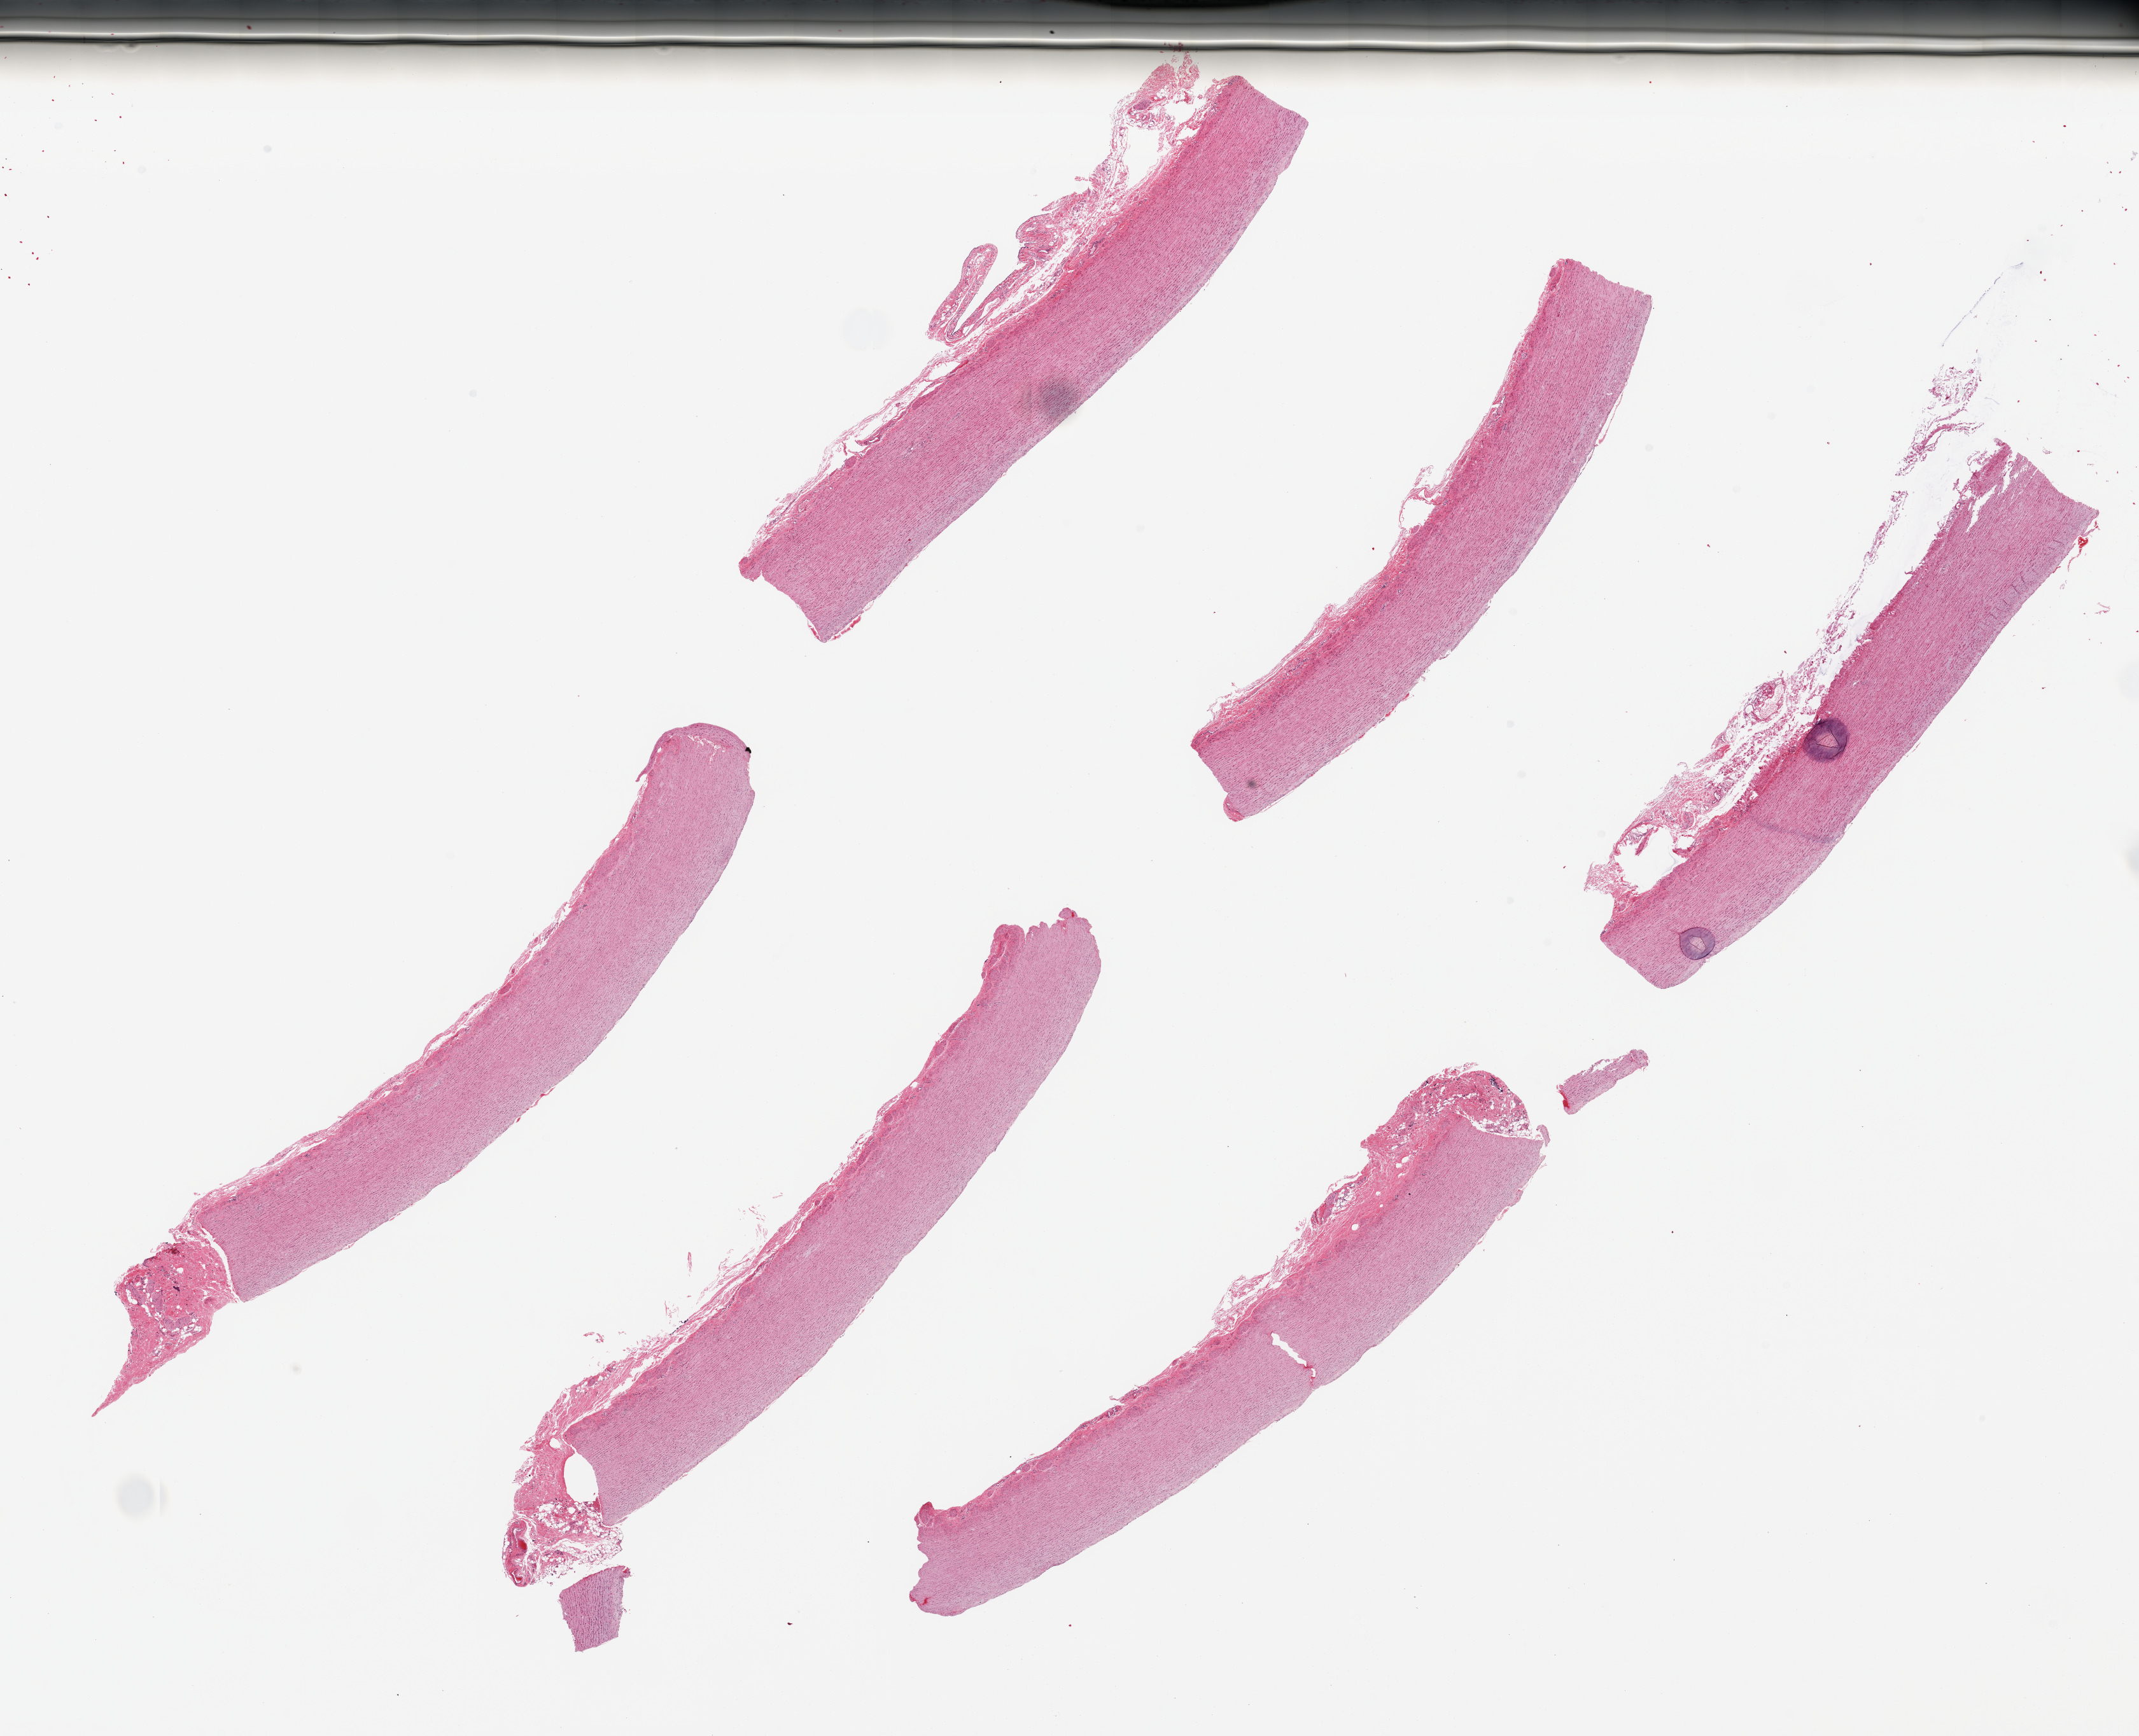
Digitized haematoxylin and eosin-stained section, a low-resolution overview of the entire scanned area, about 26.6 x 21.6 mm. PAXgene-fixed paraffin-embedded (PFPE) section. Section of aorta (target tissue). Donor tissue sample.
* review note (as recorded): 6 pieces, 10x1.5mm